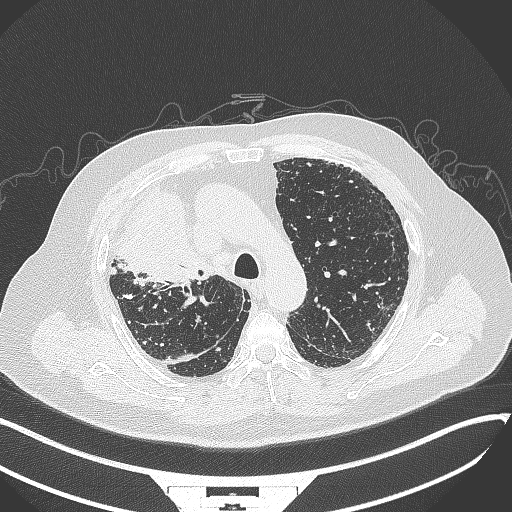
Chest CT, one axial slice. Slice 254 of 384 in the series (ordered by position). Reconstruction kernel B70f. Lung window (W 1500 / L -600 HU). 1 mm slice thickness. 512 × 512 image matrix. Male patient, age 69 years. From the clinical record (not read from this slice): clinical TNM (as recorded): T4 N3 M1.
Annotated regions visible in this slice (rectangle marked by the reading radiologist):
- lung tumour (recorded histology: adenocarcinoma): bounding box (x1, y1, x2, y2) in pixels: (107, 185, 204, 286)